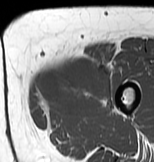
MRI of an extremity soft-tissue mass, one axial slice. Position 19 of 83 along the scan axis. MR volume resampled by the dataset authors to the PET/CT grid (not the native acquisition matrix). 3.27 mm slice thickness. 154 × 162 image matrix, field of view 150 × 158 mm. Female patient. From the clinical record (not read from this slice): histological type: myxofibrosarcoma; grade: intermediate; site of the primary tumour: left thigh.
Structures marked on this image (expert contour drawn on MRI and transferred to this co-registered scan by the dataset authors):
- gross tumour volume including surrounding oedema: box from (x=33, y=55) to (x=111, y=120) px
- gross tumour volume (mass): (x=35, y=57)–(x=109, y=120)